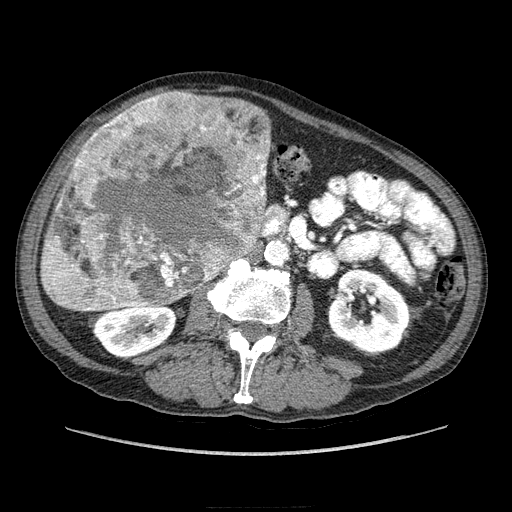
Contrast-enhanced abdominal CT (liver protocol), one axial slice; position 81 of 218 along the scan axis; soft-tissue window (W 400 / L 40 HU); 2.5 mm slice thickness; 512 × 512 image matrix, field of view 380 × 380 mm. From the clinical record (not read from this slice): diagnosis: hepatocellular carcinoma (patient treated with transarterial chemoembolisation; whether this scan precedes or follows treatment is not stated here); TNM stage (as recorded): Stage-IIIA; Child-Pugh class: A; tumour nodularity: multinodular.
Outlined on this slice (semi-automatically segmented with operator editing):
- liver parenchyma outside the tumour (the mass and vessels are separate outlines, so this box may not span the whole liver): bounding box [x1, y1, x2, y2] px = [63, 150, 81, 307]
- mass: [40, 89, 271, 312]